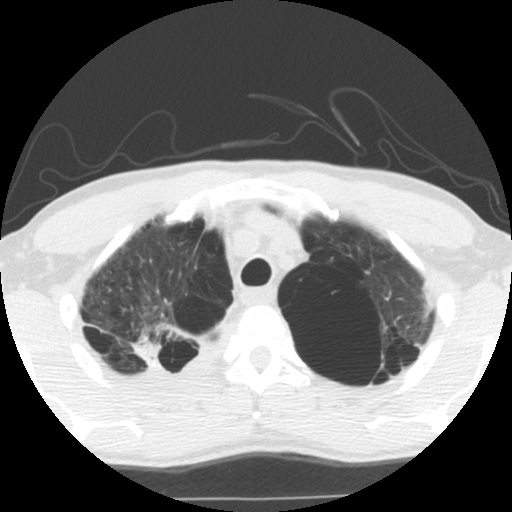
Low-dose screening chest CT, one axial slice. Slice 96 of 119 in the series (ordered by position). Reconstruction kernel STANDARD. 140 kVp. Lung window (W 1500 / L -600 HU). 2.5 mm slice thickness. 512 × 512 image matrix, field of view 295 × 295 mm.
Structures marked on this image (expert manual segmentation):
- lesion 1 (tumor, upper lobe of right lung): bounding box <135,324,181,363> (left, top, right, bottom; pixels)